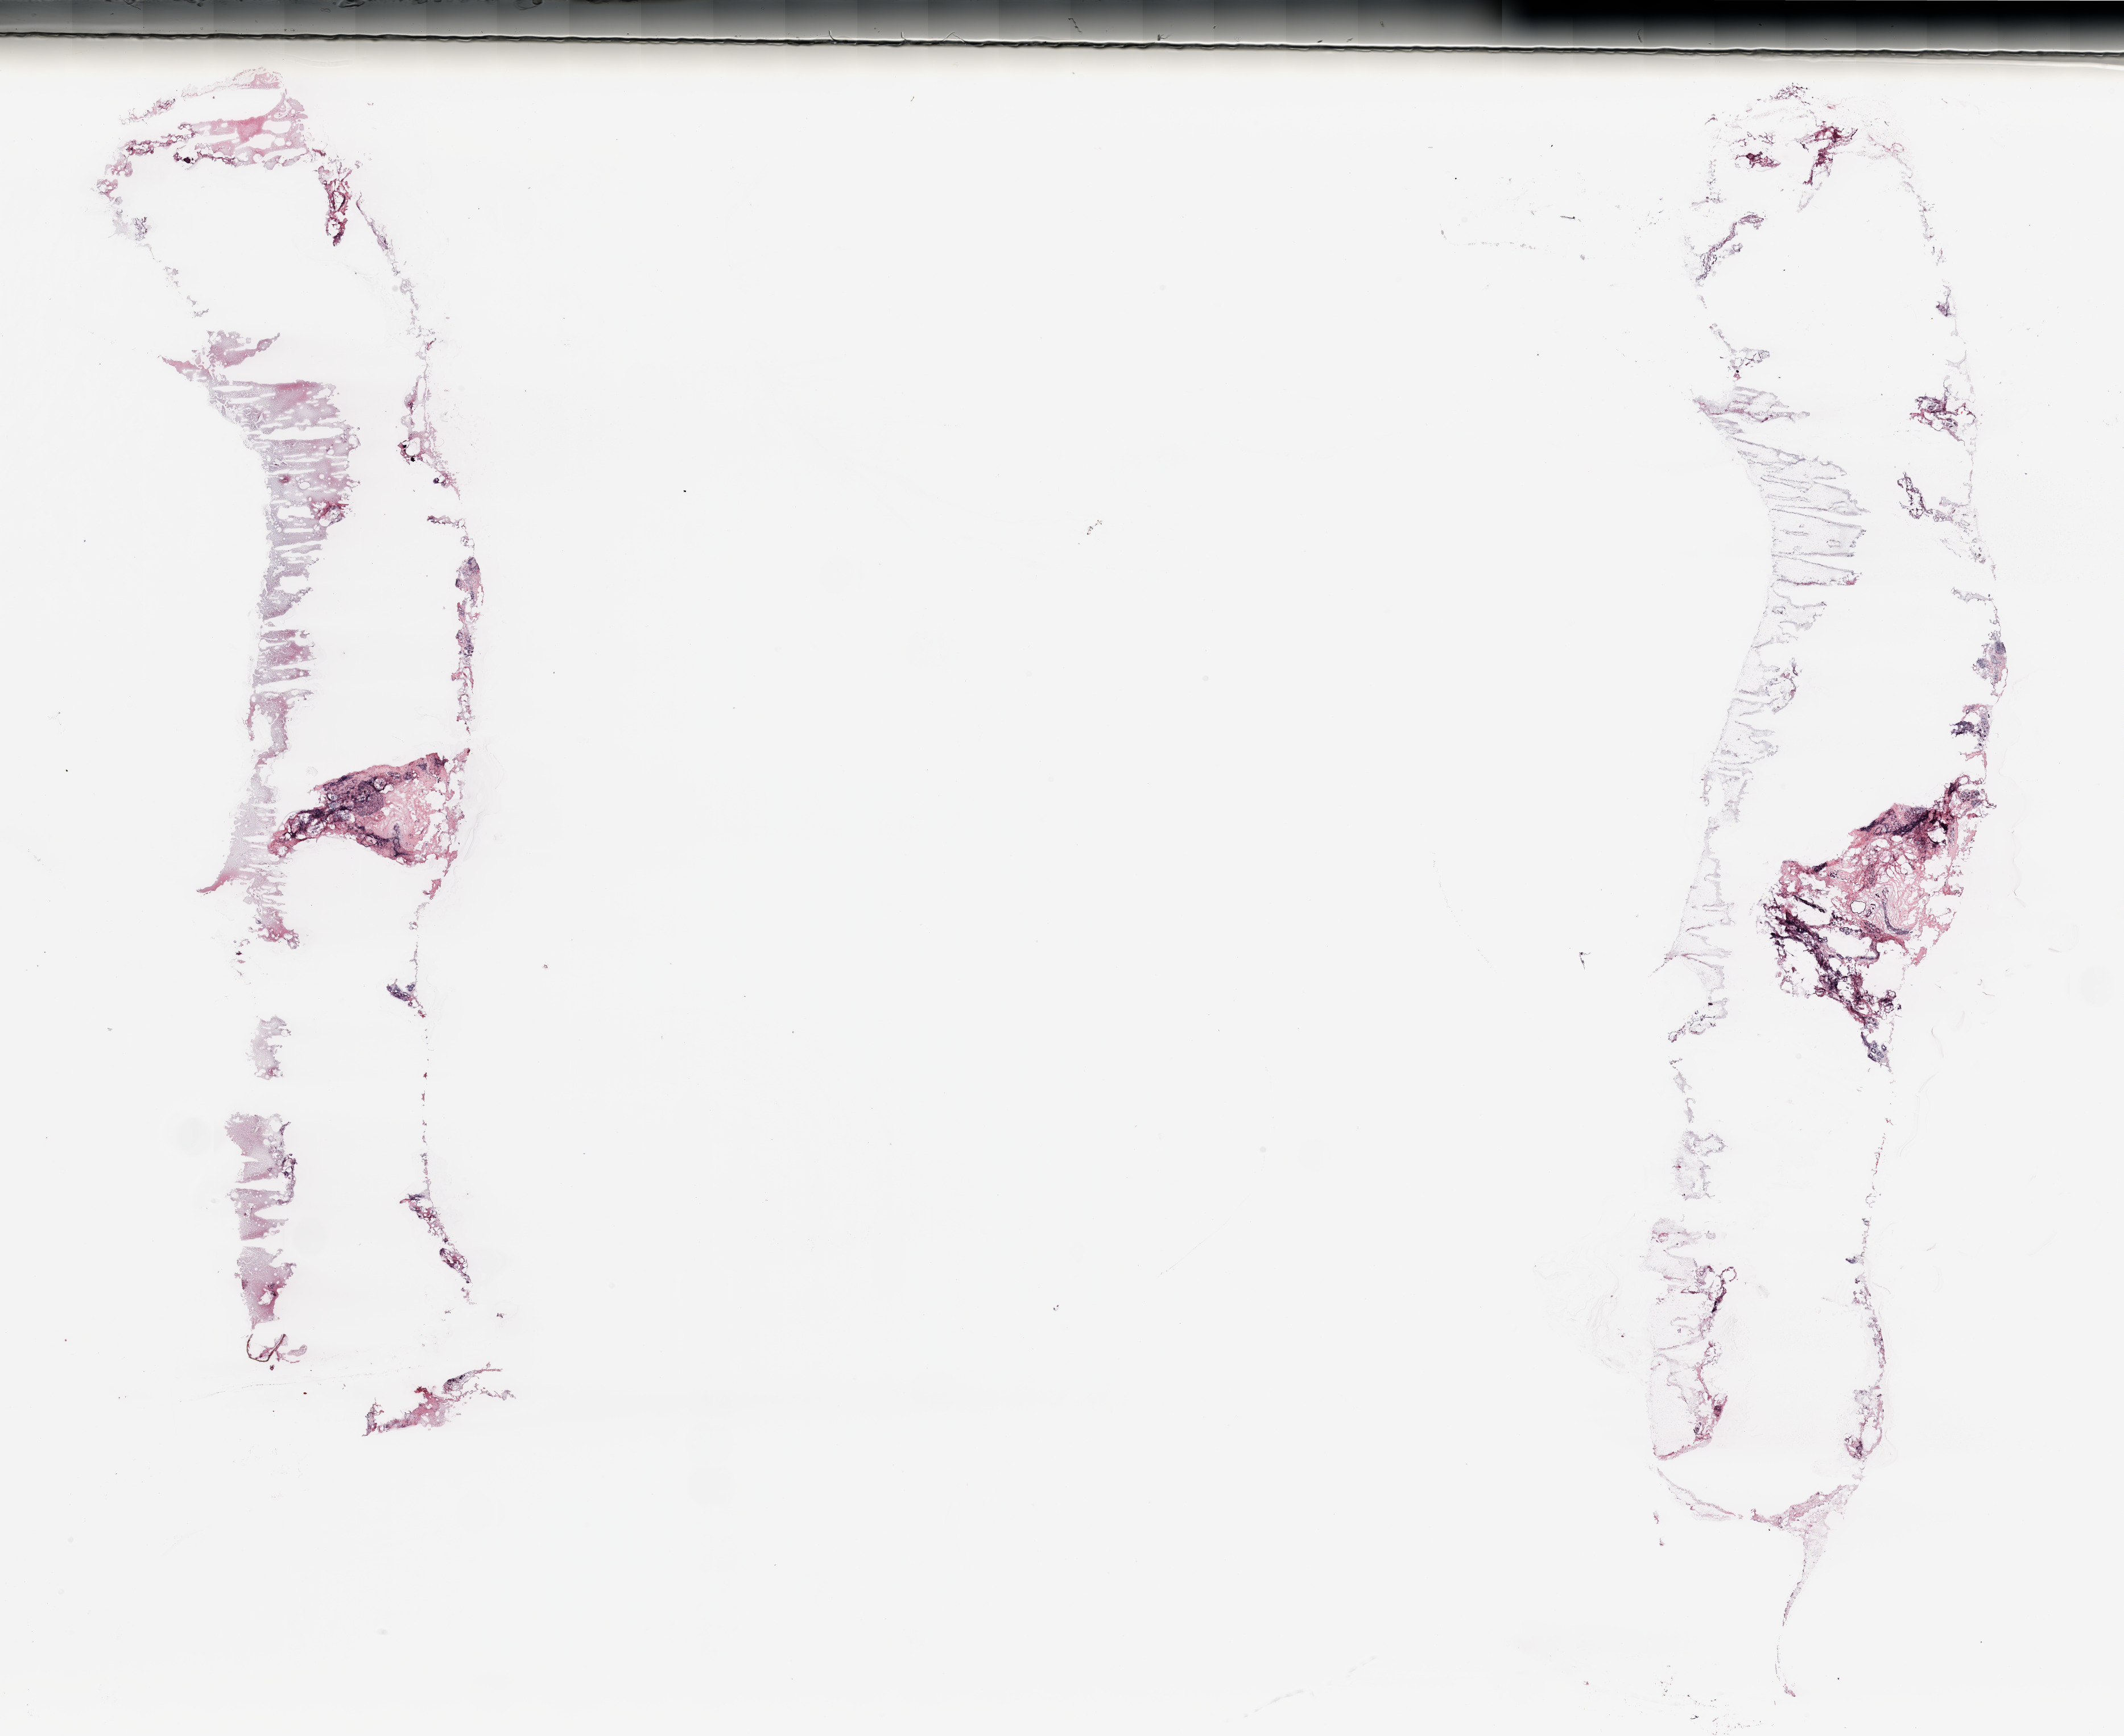
Whole-slide histology image, H&E-stained, whole scanned area (about 29.5 x 24.1 mm) shown as a low-resolution overview. Breast, tissue type not recorded.
Patient diagnosis (cohort enrolment): breast cancer (breast).